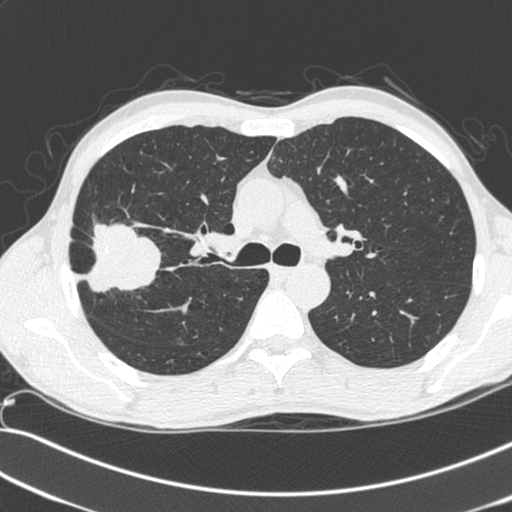
Chest CT (low-dose screening protocol), one axial image; baseline annual screen; lung window (W 1500 / L -600 HU); 1.3 mm slice thickness; standard (soft-tissue) reconstruction kernel (C); slice 85 of 281 in the series. Male, age 55 years at enrolment.
- Expert reader's lesion annotation, box from (x=69, y=225) to (x=155, y=301) px.
- The exam's reader record, not a measurement of the box and not confirmed to be the same lesion: non-calcified nodule or mass ≥4 mm, right upper lobe, 52 × 39 mm, spiculated (stellate) margins, soft tissue attenuation.
- Official screen result: positive, change unspecified: nodule(s) >= 4 mm or enlarging nodule(s), mass(es), or other non-specific abnormalities suspicious for lung cancer.
- Lung cancer was diagnosed 25 days after this screen: large cell neuroendocrine carcinoma, right upper lobe, poorly differentiated (G3), stage IIB (AJCC 6th edition), 49 mm at pathology.